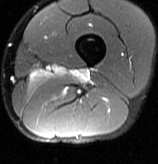
MRI of an extremity soft-tissue mass, one axial slice. Slice 16 of 70 in the series (ordered by position). T2-weighted fat-saturated. MR volume resampled by the dataset authors to the PET/CT grid (not the native acquisition matrix). 3.27 mm slice thickness. 158 × 164 image matrix, field of view 154 × 160 mm. Male patient. Case-level facts recorded for this patient, not image findings: histological type: extraskeletal osteosarcoma; grade: high; site of the primary tumour: left adductur.
Outlined on this slice (expert contour drawn on MRI and transferred to this co-registered scan by the dataset authors):
- gross tumour volume (mass): bounding box (x1, y1, x2, y2) in pixels: (72, 69, 89, 81)